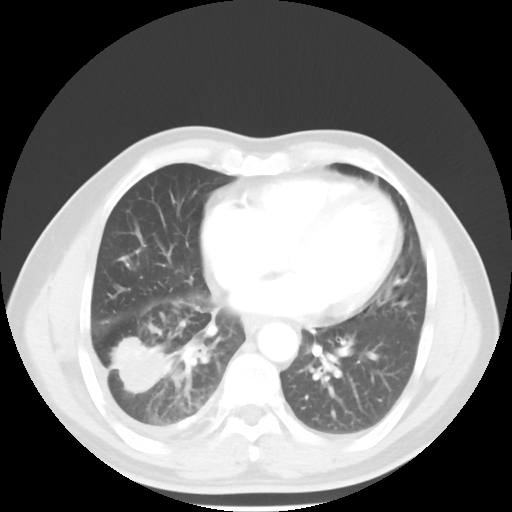
Chest CT, one axial slice. Reconstruction kernel STANDARD. Lung window (W 1500 / L -600 HU). 512 × 512 image matrix. Male patient, age 56 years. From the clinical record (not read from this slice): clinical TNM (as recorded): T2 N3 M1.
Annotated regions visible in this slice (rectangle marked by the reading radiologist):
- lung tumour (recorded histology: adenocarcinoma): bounding box (x1, y1, x2, y2) in pixels: (109, 329, 173, 398)